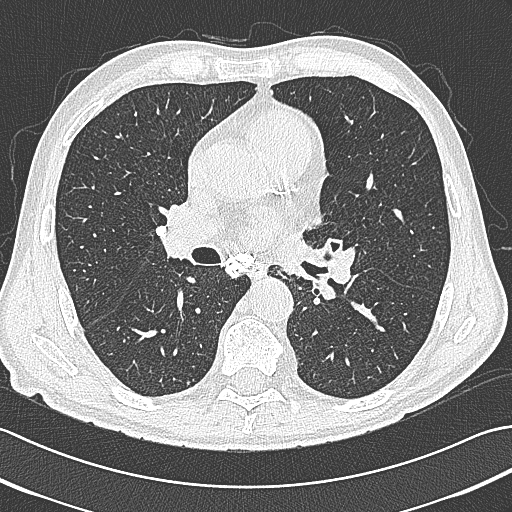
Low-dose screening chest CT, axial slice; first (baseline) screen; lung window (W 1500 / L -600 HU); 1 mm slice thickness; lung (sharp) reconstruction kernel (B80f); 120 kVp. Male, age 65 years at enrolment. Current smoker at enrolment.
- Expert reader's lesion annotation, bounding box [x1, y1, x2, y2] px = [304, 232, 352, 275].
- Screening reader's record for this exam: no non-calcified nodule ≥4 mm recorded.
- Official screen result: negative screen, minor abnormalities not suspicious for lung cancer.
- Participant outcome: lung cancer diagnosed 161 days after this screen — large cell neuroendocrine carcinoma, left hilum, left main stem bronchus, stage IIIB (AJCC 6th edition), 70 mm at pathology.